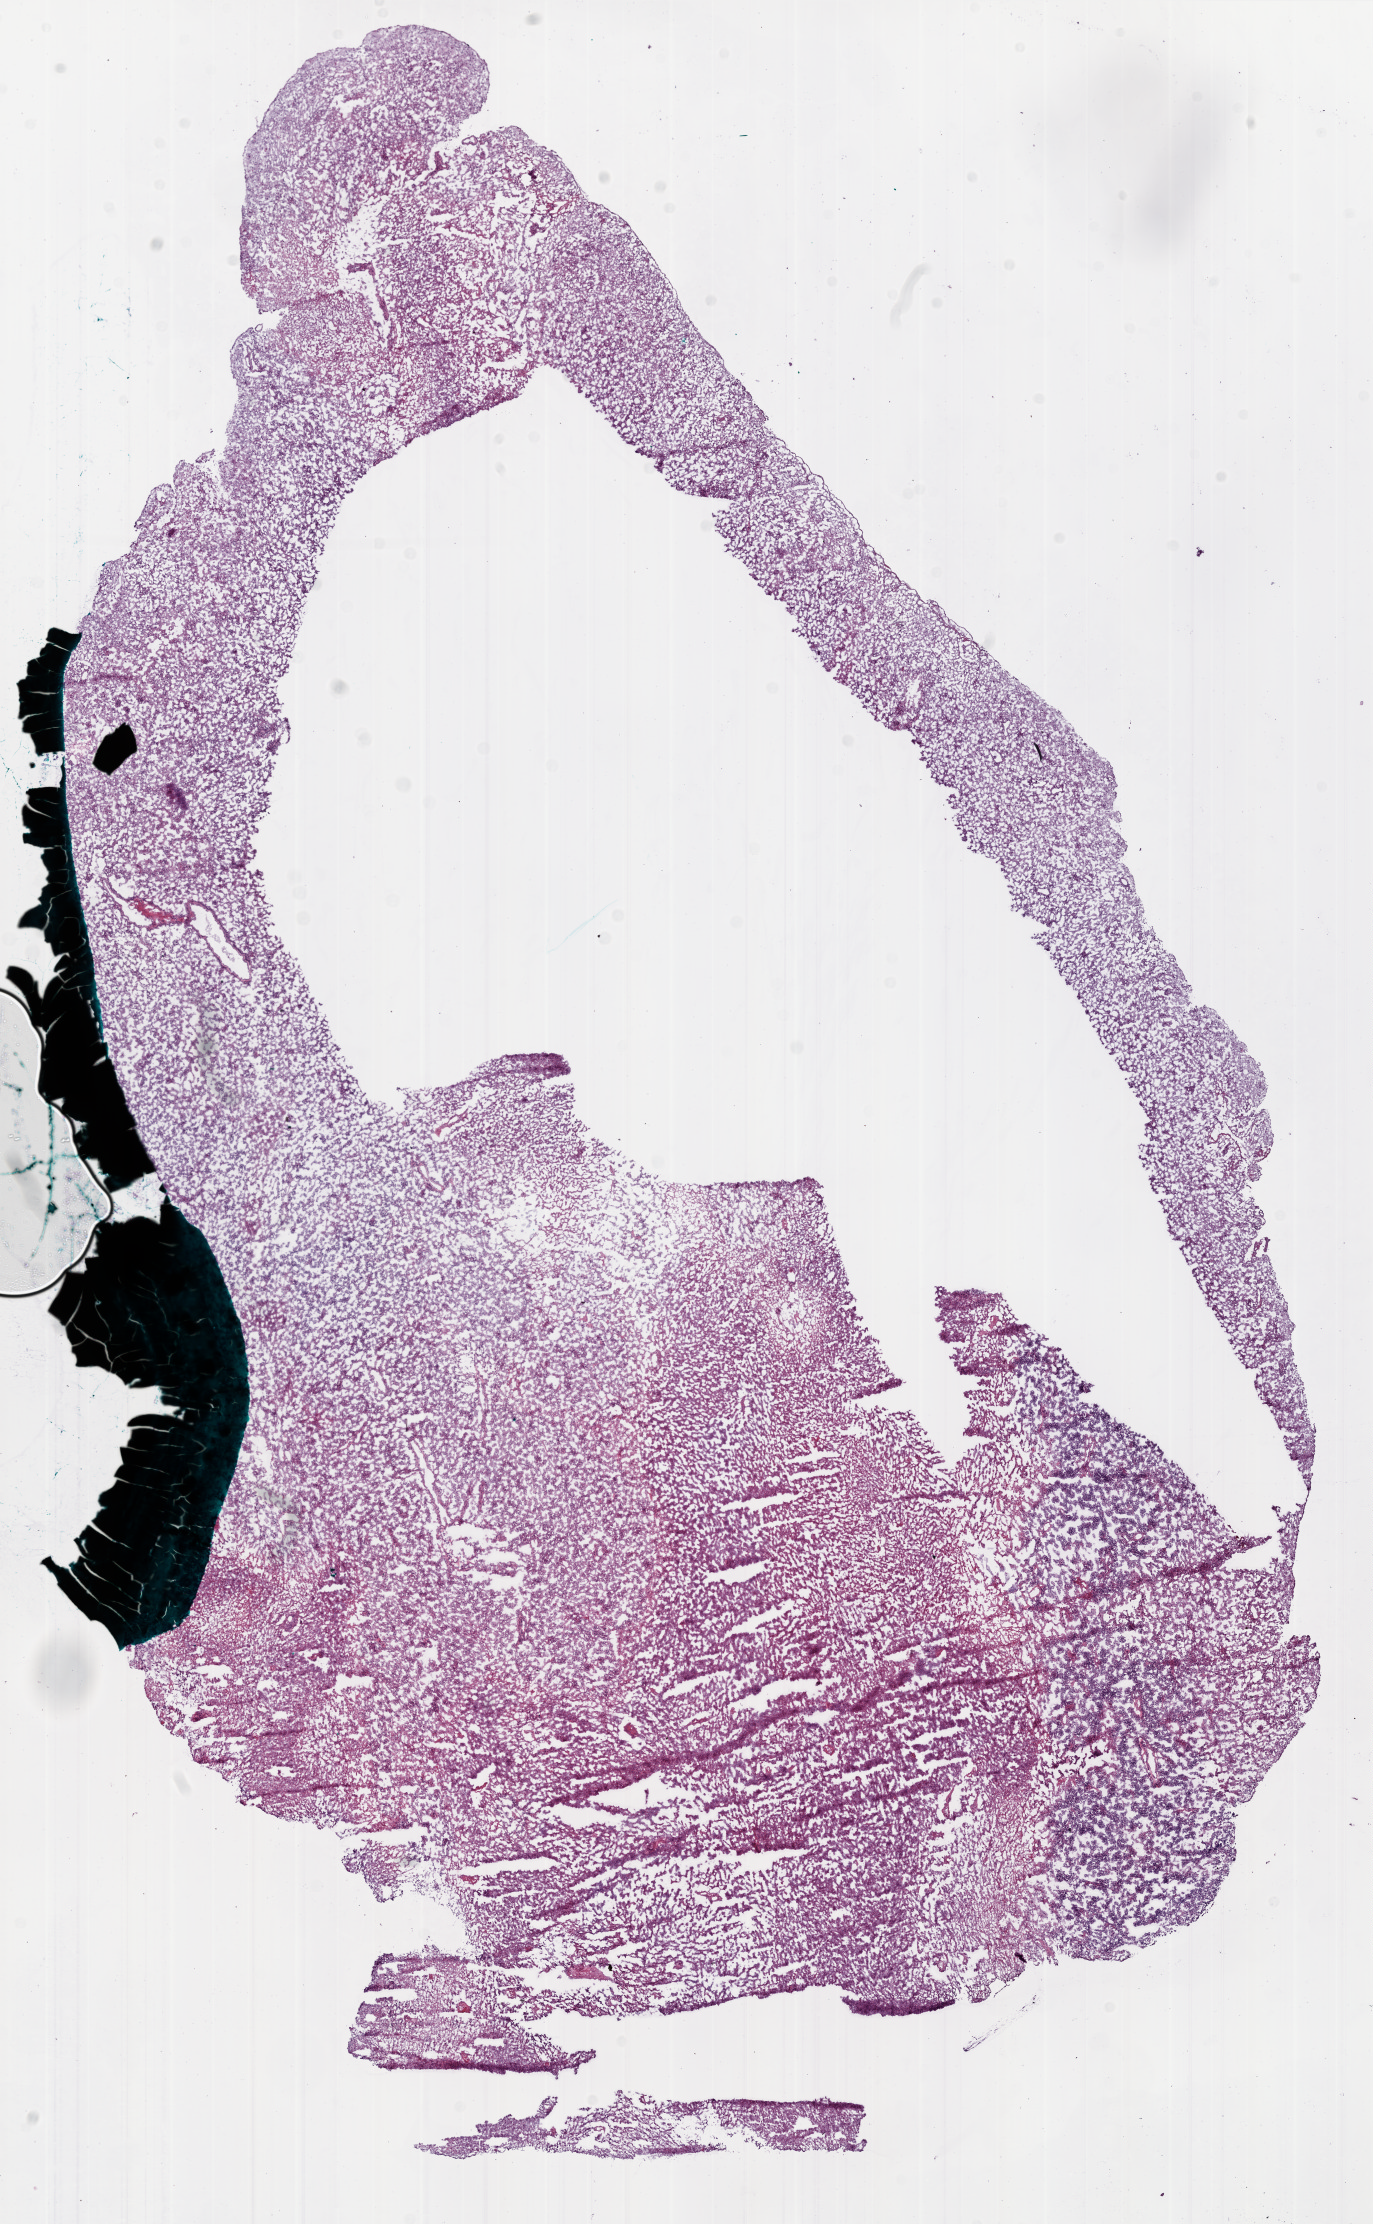
Hematoxylin and eosin (H&E) stained whole-slide image — a low-resolution overview of the entire scanned area, about 11.0 x 17.8 mm (slide scanned at 20x), frozen section, sample: primary tumour, brain. Male patient; age at initial diagnosis 74 years. Slide review estimates, as recorded: tumour cells 70%, tumour nuclei 100%, normal cells 0%, stromal cells 0%, necrosis 30%. Inflammatory infiltration, as recorded: lymphocyte infiltration 0%.
* pathologic diagnosis: Glioblastoma